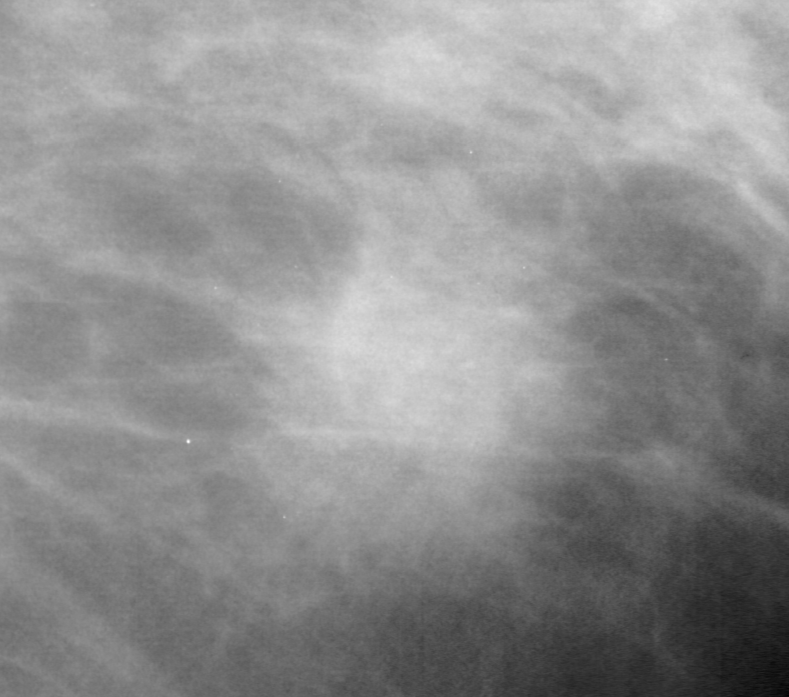
Crop from a digitized film mammogram around one marked abnormality; right breast; MLO view; BI-RADS breast density category 3 (scale 1–4).
Finding: calcifications, morphology pleomorphic, distribution clustered; BI-RADS assessment category 5; pathology (as recorded): malignant.